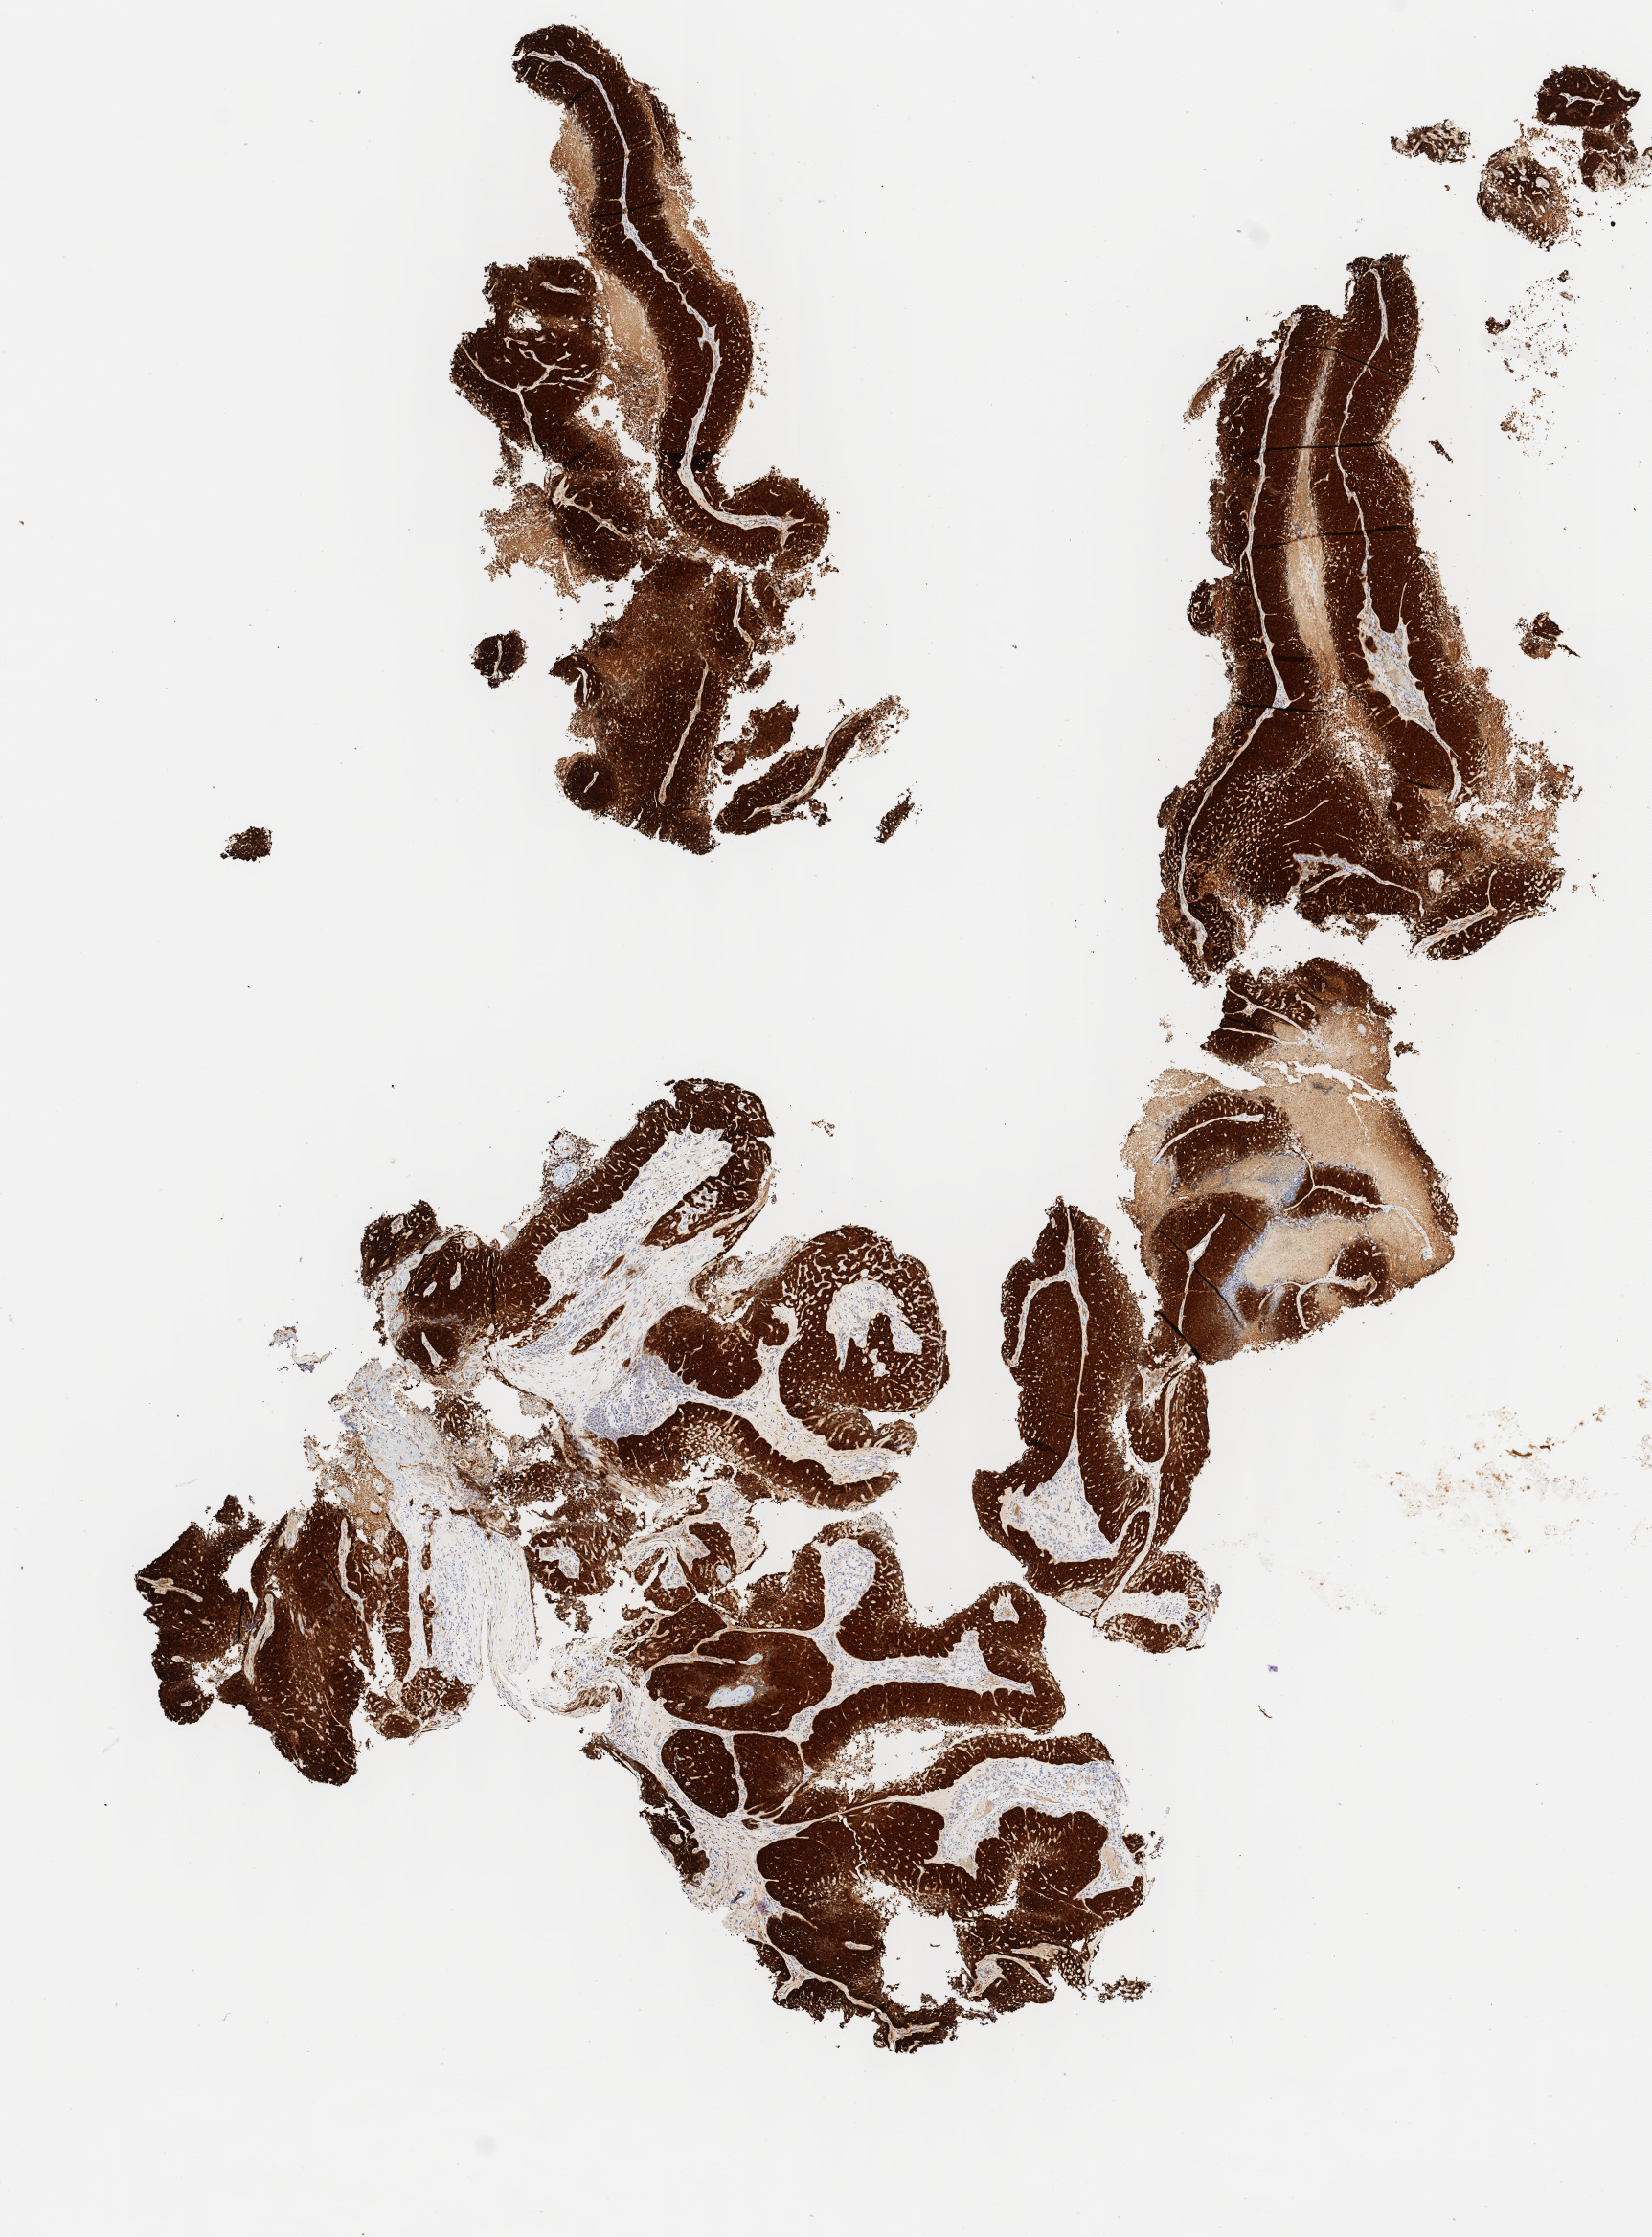
Immunohistochemistry (IHC) whole-slide image stained for p16 (p16INK4a), low-resolution overview of the scanned area, about 6.9 x 9.3 mm, tumor tissue, anatomic site: cervix. Patient: female, age 64 years.
Diagnosis: Squamous cell carcinoma, large cell, nonkeratinizing, NOS.